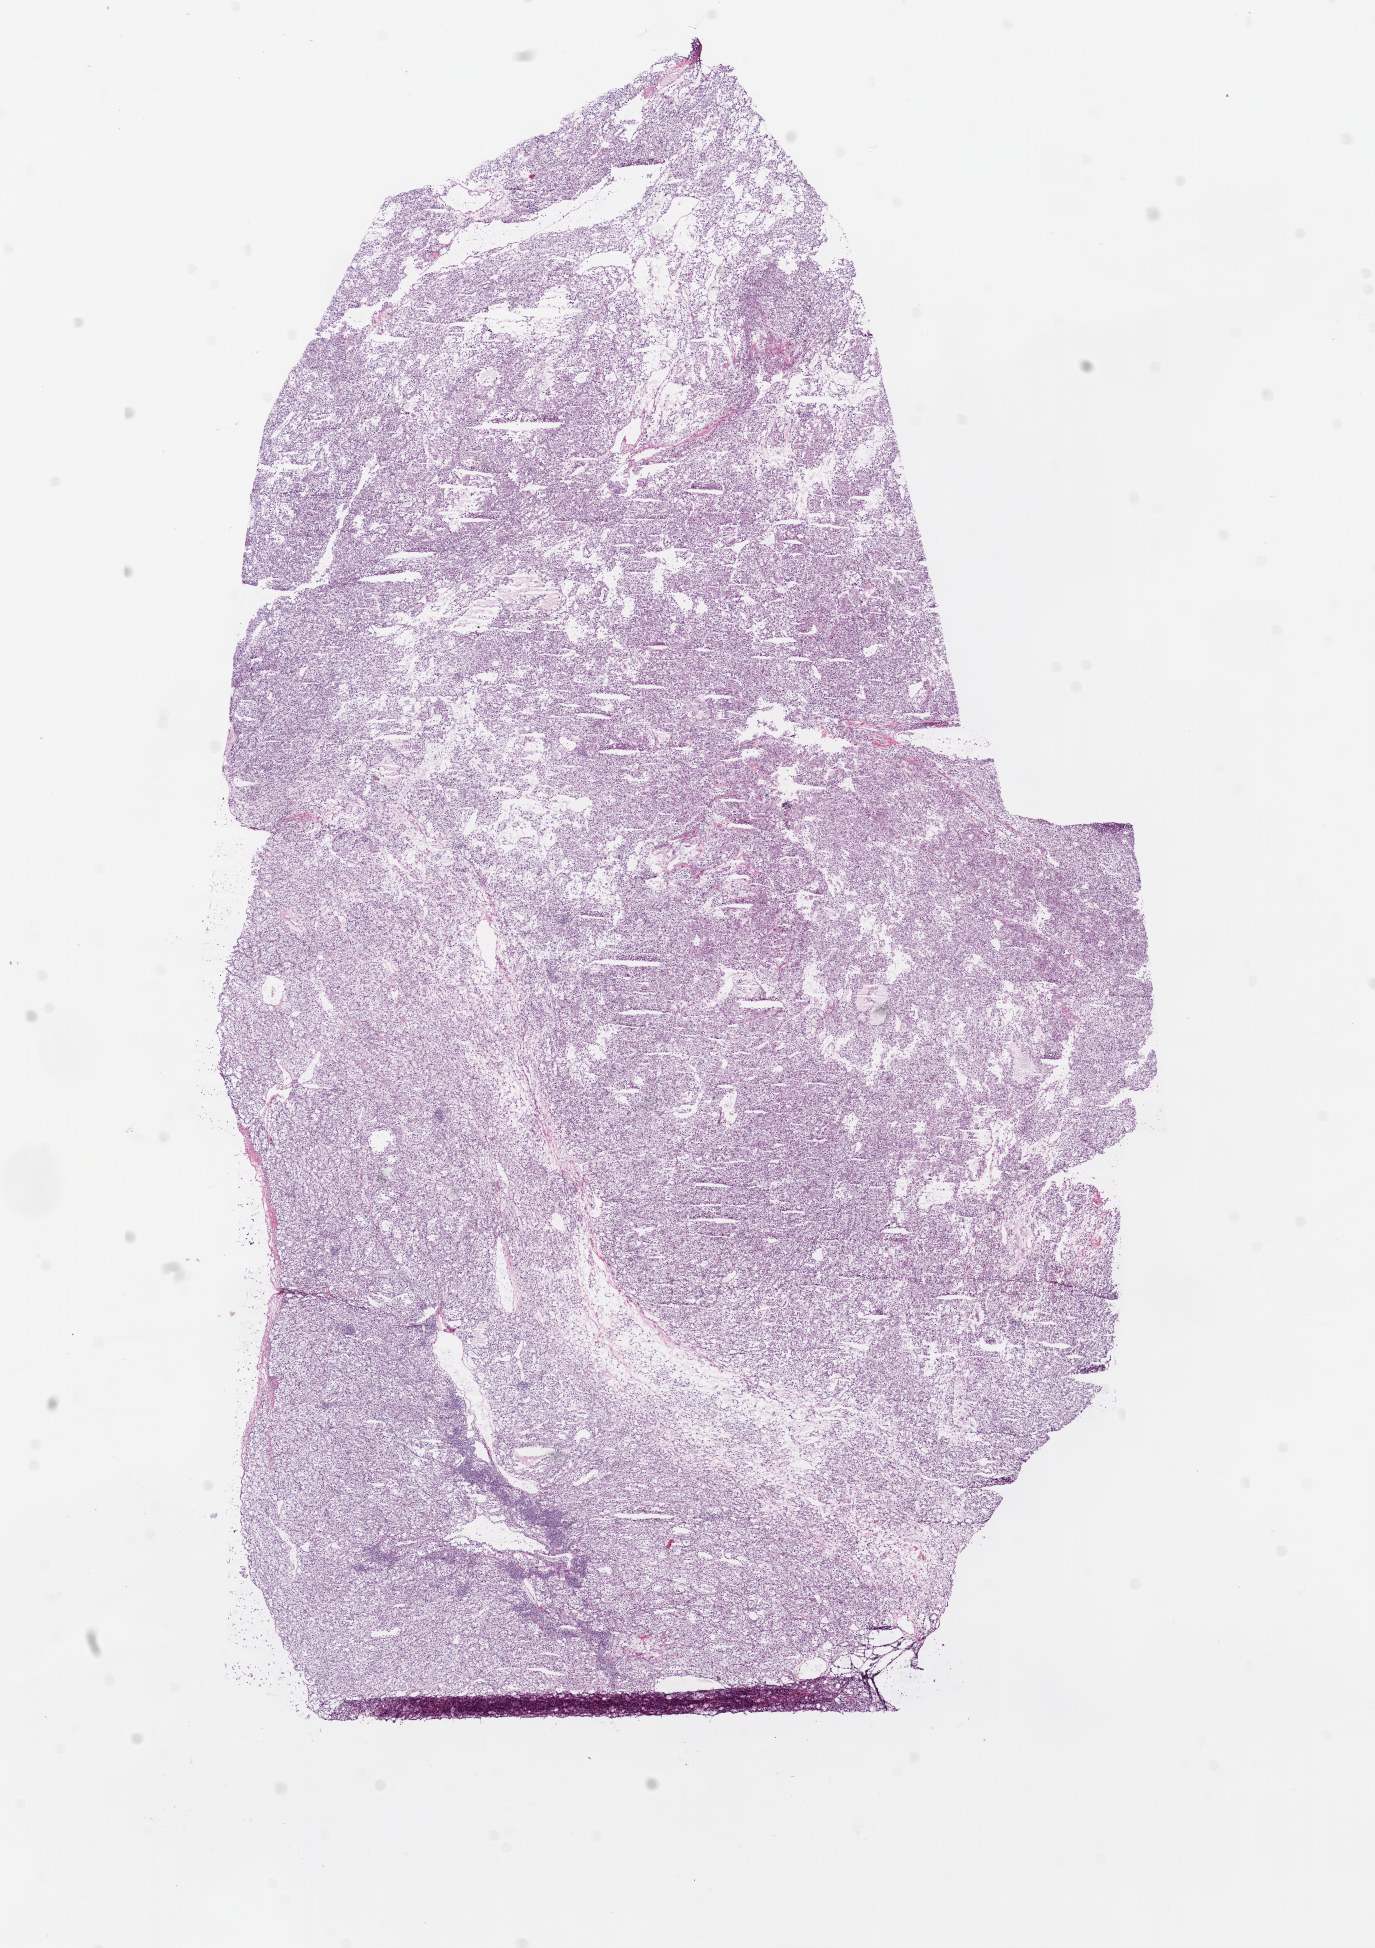
H&E-stained whole-slide image — whole scanned area (about 11.0 x 15.6 mm, slide scanned at 20x) shown as a low-resolution overview. Frozen section. Sample: primary tumour, kidney. Male patient; age at initial diagnosis 73 years. Histologic grade: G2 (moderately differentiated). Pathologist review of this section (percent, as recorded): tumour cells 95%, tumour nuclei 90%, normal cells 0%, stromal cells 5%, necrosis 0%.
• AJCC pathologic stage: I
• laterality: left
• diagnosis: Clear cell adenocarcinoma, NOS